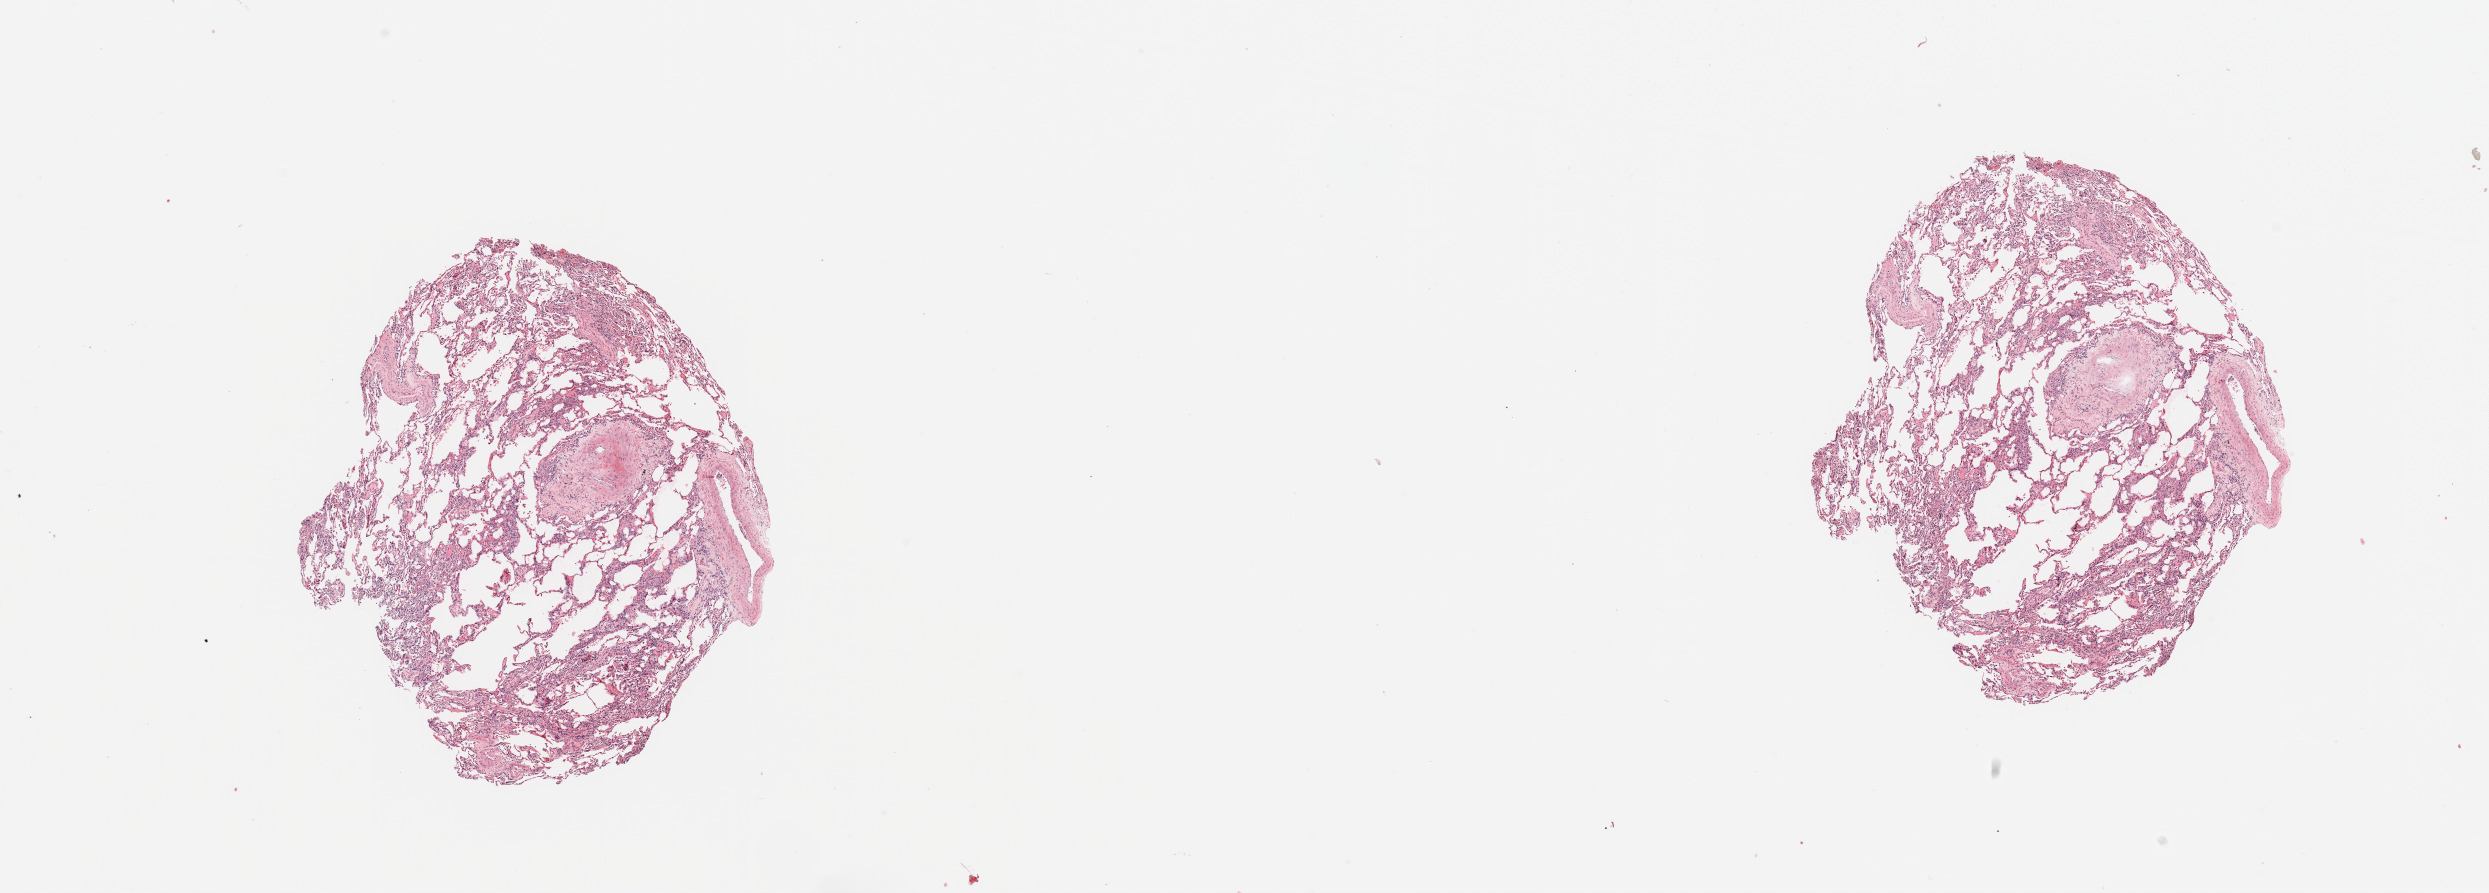
H&E whole-slide image, shown as a low-resolution overview of the whole scanned area (about 19.7 x 7.1 mm, from a 20x scan); normal (non-tumour) tissue sample, sampled site: lung. 61-year-old male patient.
- this section: normal (non-tumour) tissue from the same patient
- patient diagnosis: Squamous cell carcinoma, NOS